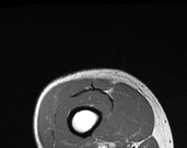
MRI of an extremity soft-tissue mass, one axial slice. Slice 26 of 114 in the series (ordered by position). MR volume resampled by the dataset authors to the PET/CT grid (not the native acquisition matrix). 3.27 mm slice thickness. 187 × 148 image matrix. Male patient. Case-level facts recorded for this patient, not image findings: histological type: pleiomorphic leiomyosarcoma; grade: intermediate; site of the primary tumour: right thigh.
Structures marked on this image (expert contour drawn on MRI and transferred to this co-registered scan by the dataset authors):
- gross tumour volume including surrounding oedema: bounding box [x1, y1, x2, y2] px = [96, 82, 106, 87]